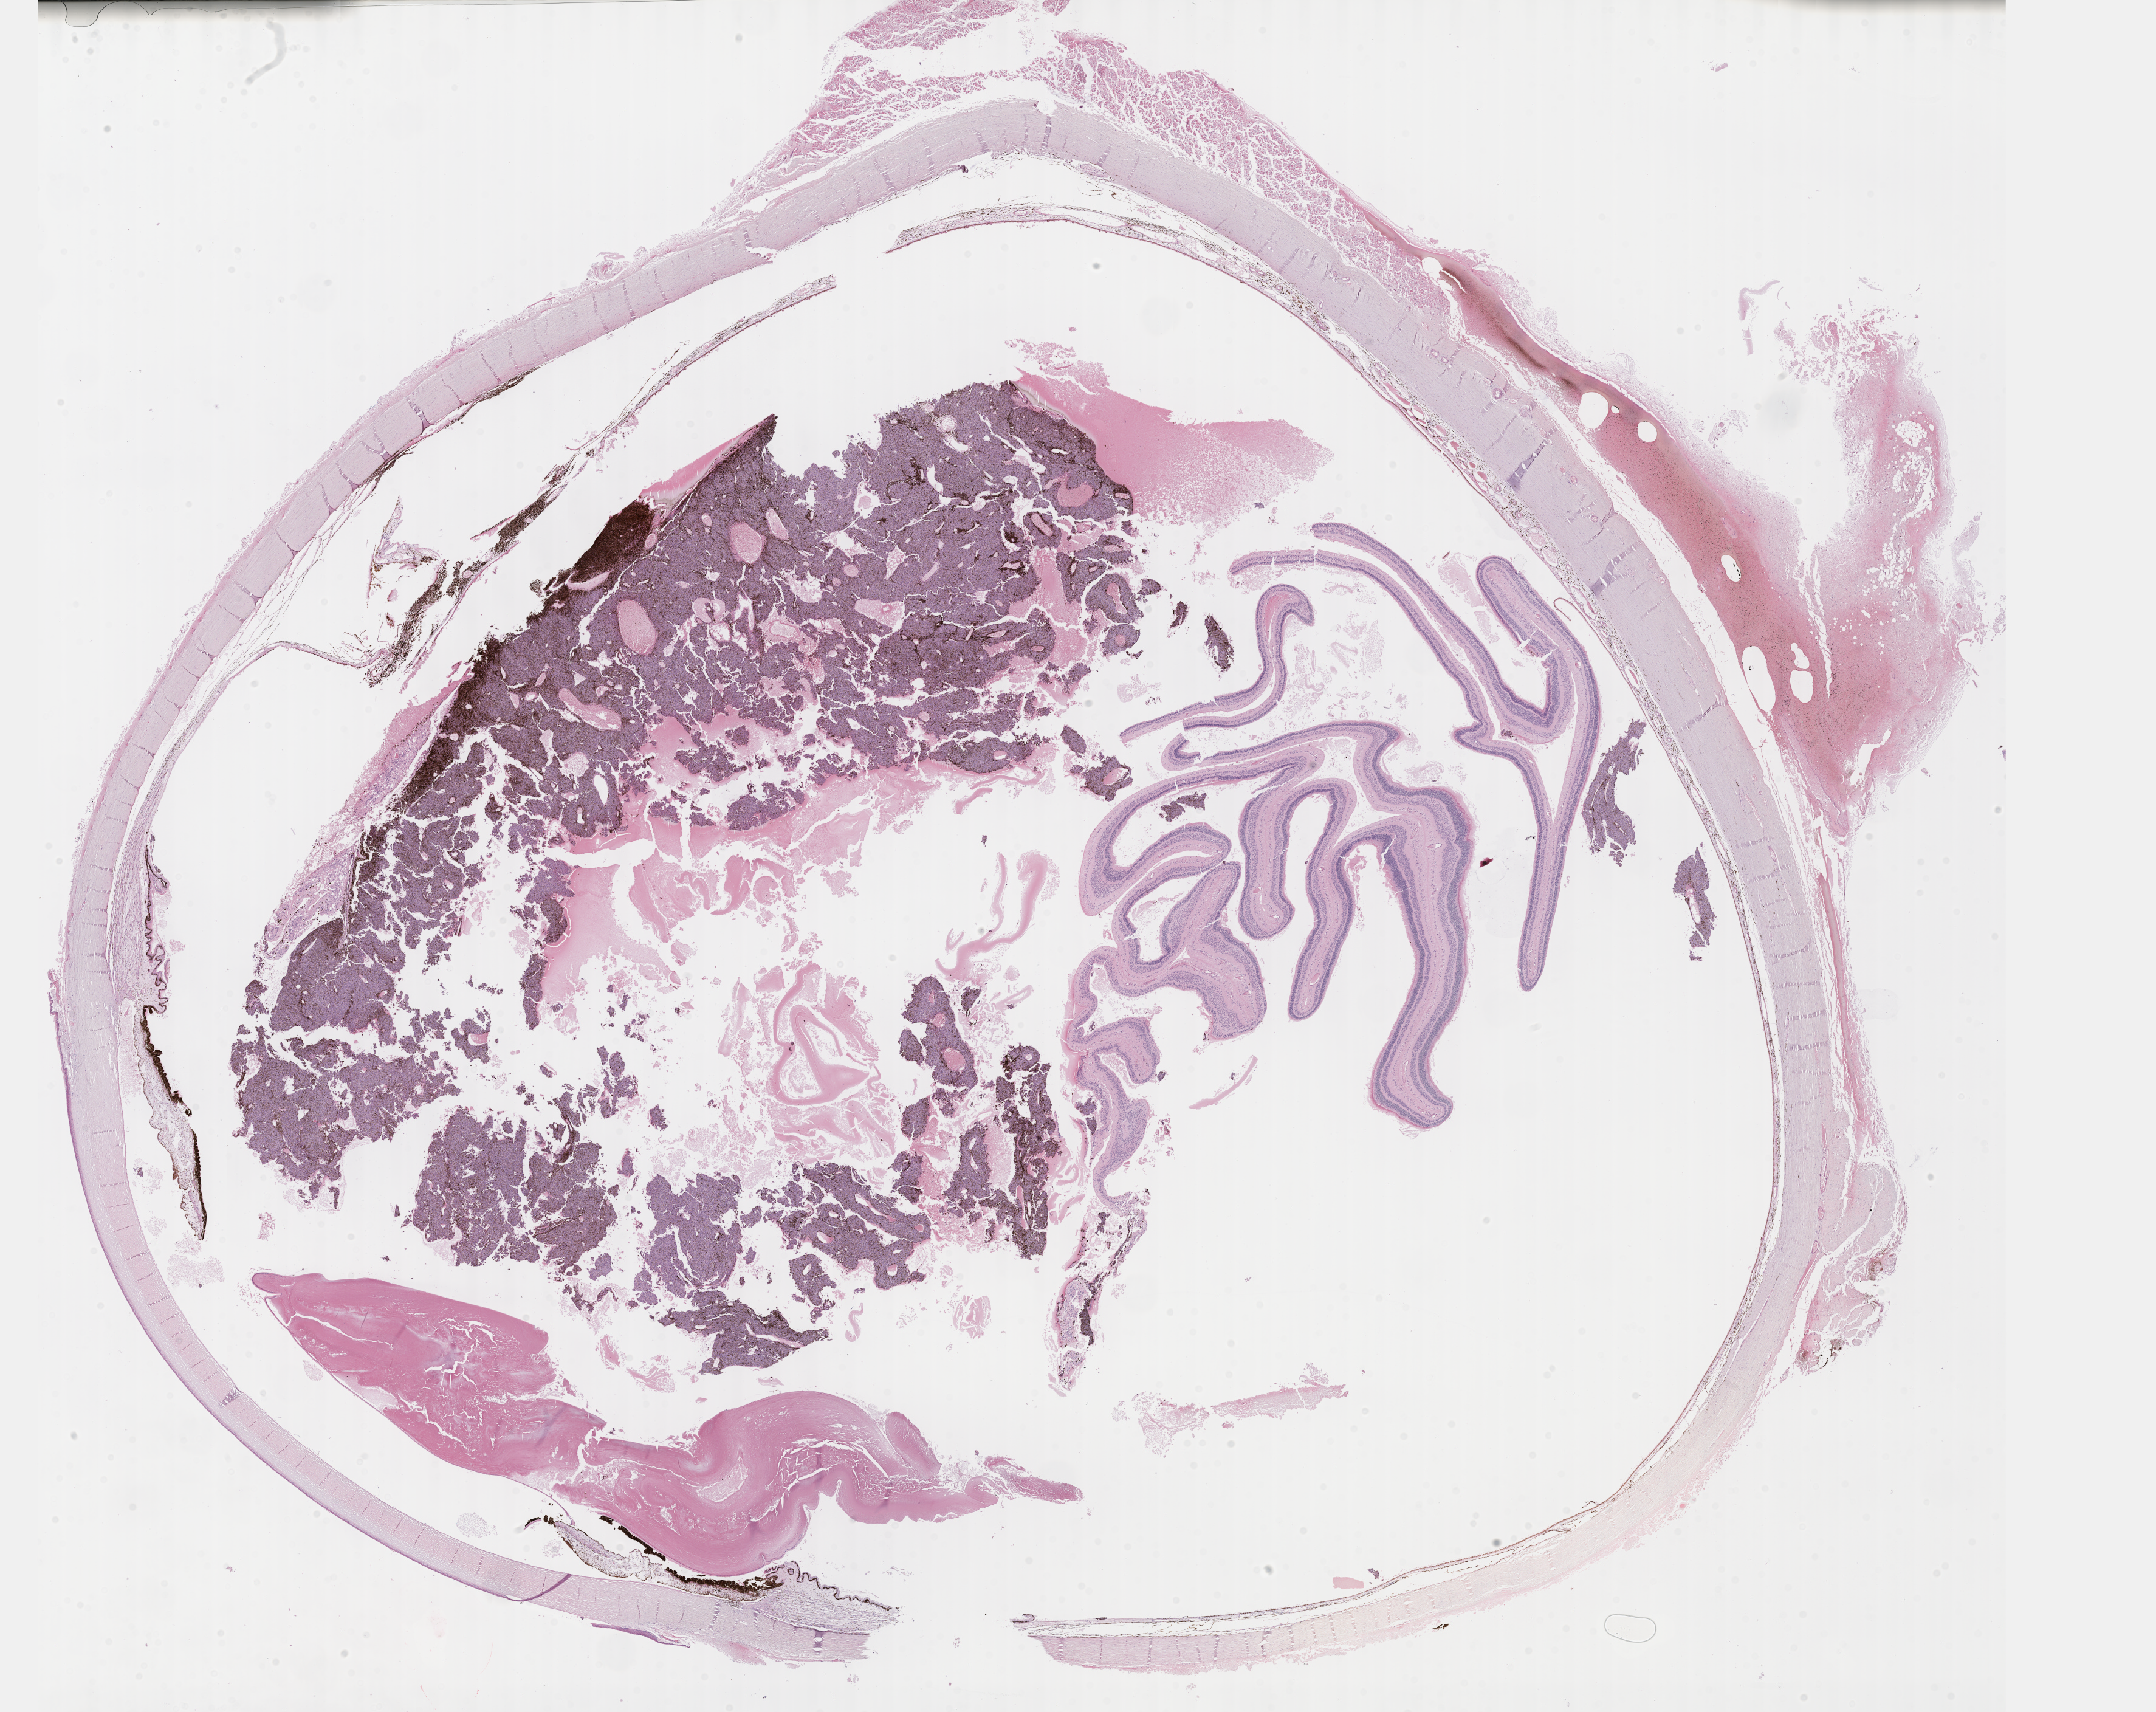
Digitized H&E tissue section (whole slide) — low-resolution overview of the scanned area, about 28.7 x 22.8 mm; formalin-fixed paraffin-embedded (FFPE) diagnostic section; sample: primary tumour, uvea. Male patient; age at initial diagnosis 50 years.
AJCC pathologic stage: IIIA. Diagnosis: Spindle cell melanoma, NOS (choroid).